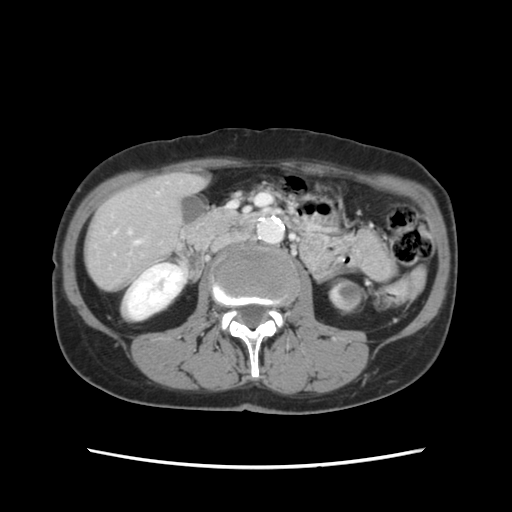
Contrast-enhanced abdominal CT, one axial slice; slice 34 of 120 in the series (ordered by position); soft-tissue window (W 400 / L 40 HU); 512 × 512 image matrix. Female patient, age 70 years. Case-level facts recorded for this patient, not image findings: diagnosis: colorectal cancer liver metastases, imaged before liver resection; multiple liver metastases: no; largest metastasis: 2.5 cm; chemotherapy before resection: yes.
Outlined on this slice (manually delineated by an expert):
- hepatic veins: box from (x=135, y=241) to (x=139, y=244) px
- liver: (x=86, y=175)–(x=202, y=289)
- planned liver remnant (the part of the liver to remain after resection): (x=86, y=174)–(x=202, y=290)
- portal vein (with intrahepatic branches): (x=128, y=231)–(x=131, y=234)